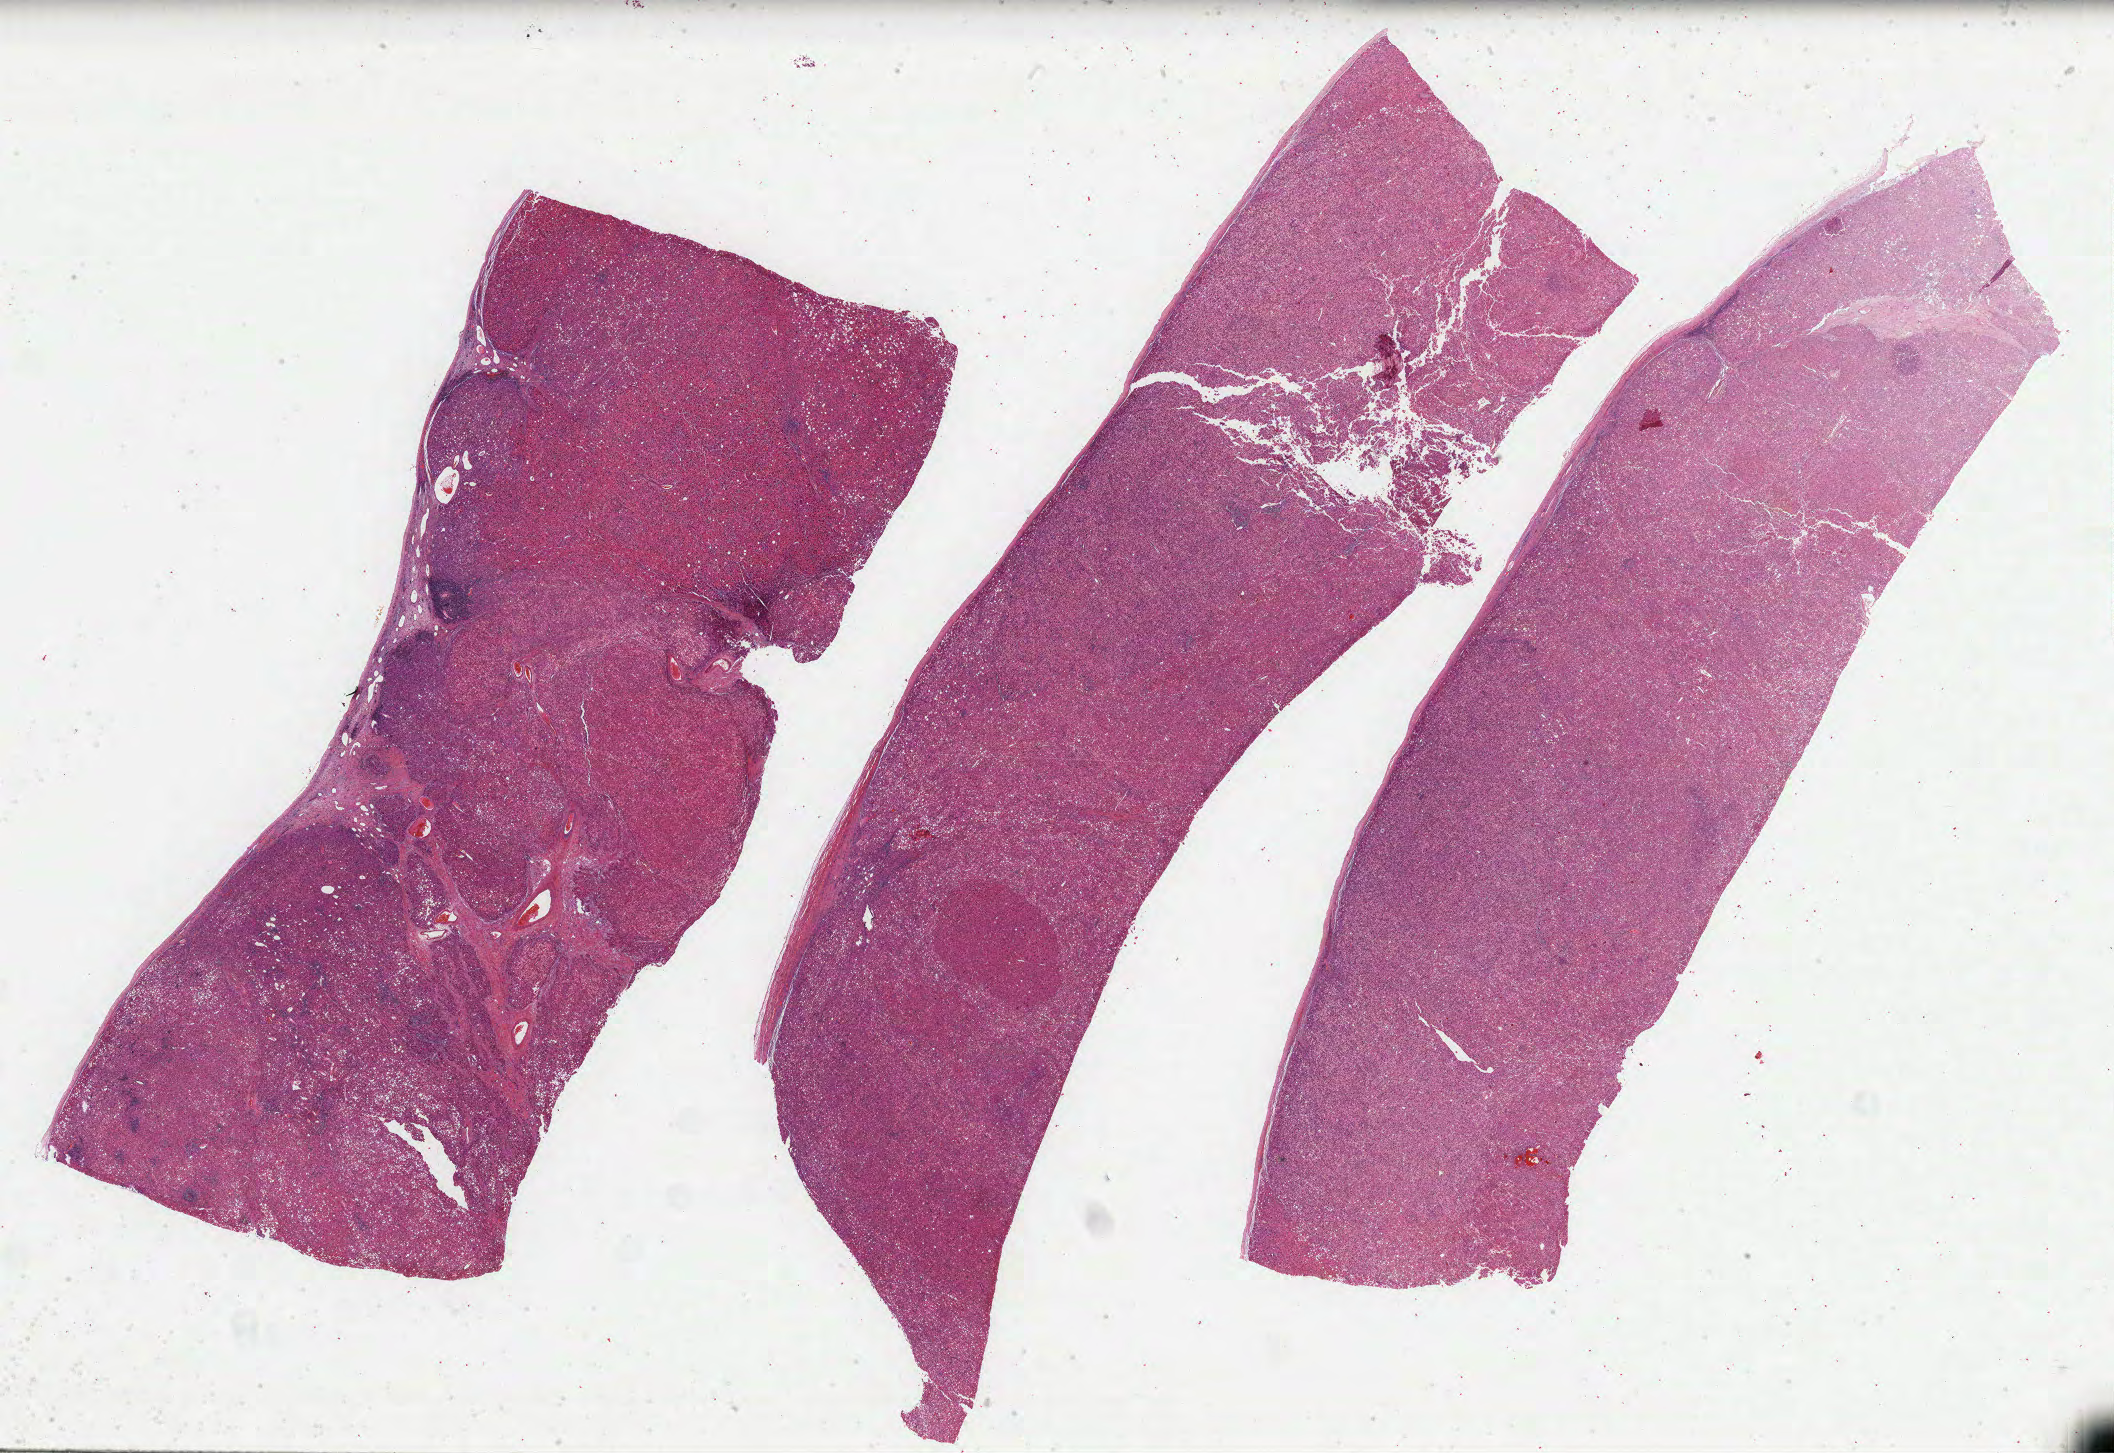
Digitized H&E-stained tissue section (whole slide) — low-resolution overview of the scanned area, about 34.2 x 23.5 mm. Formalin-fixed paraffin-embedded (FFPE) diagnostic section. Liver, primary tumour sample. Patient: female, age at initial diagnosis 68 years. Histologic grade: G2 (moderately differentiated).
- AJCC pathologic stage: I (7th edition)
- pathologic diagnosis: Hepatocellular carcinoma, NOS